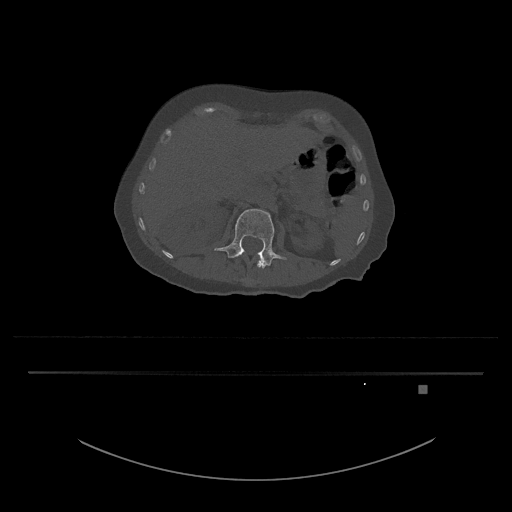
CT including the spine, one axial slice. Slice 506 of 797 in the series (ordered by position). Reconstruction kernel Br40s/3. Bone window (W 1800 / L 400 HU). 512 × 512 image matrix. Female patient, age 57 years. Case-level facts recorded for this patient, not image findings: primary cancer: cervical.
Annotated regions visible in this slice (semi-automatically segmented with operator editing):
- L1 vertebra: bounding box <244,250,265,268> (left, top, right, bottom; pixels)